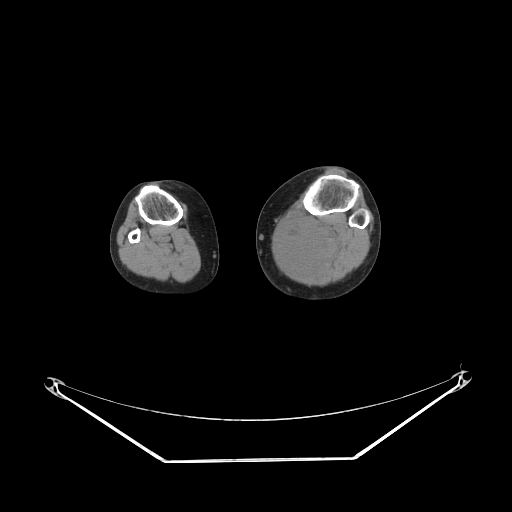
CT of an extremity soft-tissue mass (from a PET/CT study), one axial slice. Position 155 of 223 along the scan axis. Reconstruction kernel STANDARD. 140 kVp. Soft-tissue window (W 400 / L 40 HU). 3.75 mm slice thickness. 512 × 512 image matrix, field of view 500 × 500 mm. Female patient. Case-level facts recorded for this patient, not image findings: histological type: extraskeletal high grade osteogenic sarcoma; grade: high; site of the primary tumour: left calf.
Annotated regions visible in this slice (expert contour drawn on MRI and transferred to this co-registered scan by the dataset authors):
- gross tumour volume (mass): bounding box [x1, y1, x2, y2] px = [276, 221, 339, 275]